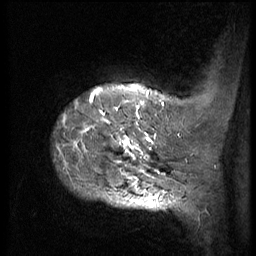
Breast MRI (dynamic contrast-enhanced), one sagittal slice; position 8 of 56 along the scan axis; 3 images stored at this slice position (order not interpretable as contrast timing); 1.5 T; TE 4.2 ms, TR 9 ms; 2.5 mm slice thickness; 256 × 256 image matrix. Patient: female, 49 years. From the clinical record (not read from this slice): setting: breast cancer imaged before/during neoadjuvant chemotherapy; receptor status: HER2-positive.
Annotated regions visible in this slice (semi-automatically segmented with operator editing):
- analysis volume of interest (the breast-tissue region the enhancement analysis was run in; not a lesion): bounding box (x1, y1, x2, y2) in pixels: (50, 85, 168, 207)
- tumour enhancement mask (voxels above the 140 % enhancement threshold inside the analysis volume of interest): (58, 87, 158, 204)